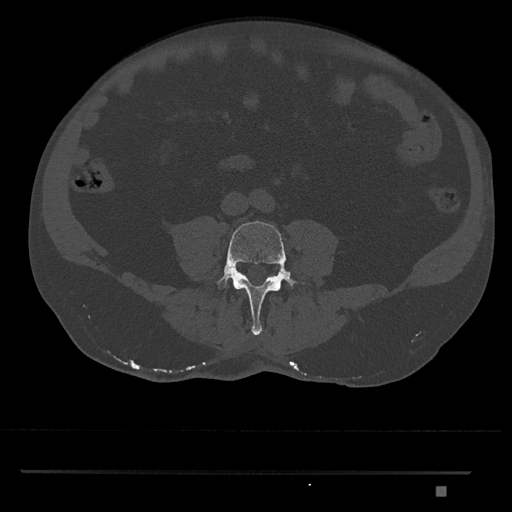
CT including the spine, one axial slice; slice 614 of 1134 in the series (ordered by position); reconstruction kernel Br40s/3; 120 kVp; bone window (W 1800 / L 400 HU); 0.5 mm slice thickness; 512 × 512 image matrix, field of view 429 × 429 mm. Patient: male, 65 years. From the clinical record (not read from this slice): primary cancer: prostate.
Structures marked on this image (semi-automatic segmentation, software-assisted and operator-edited):
- L4 vertebra: box from (x=216, y=221) to (x=310, y=336) px